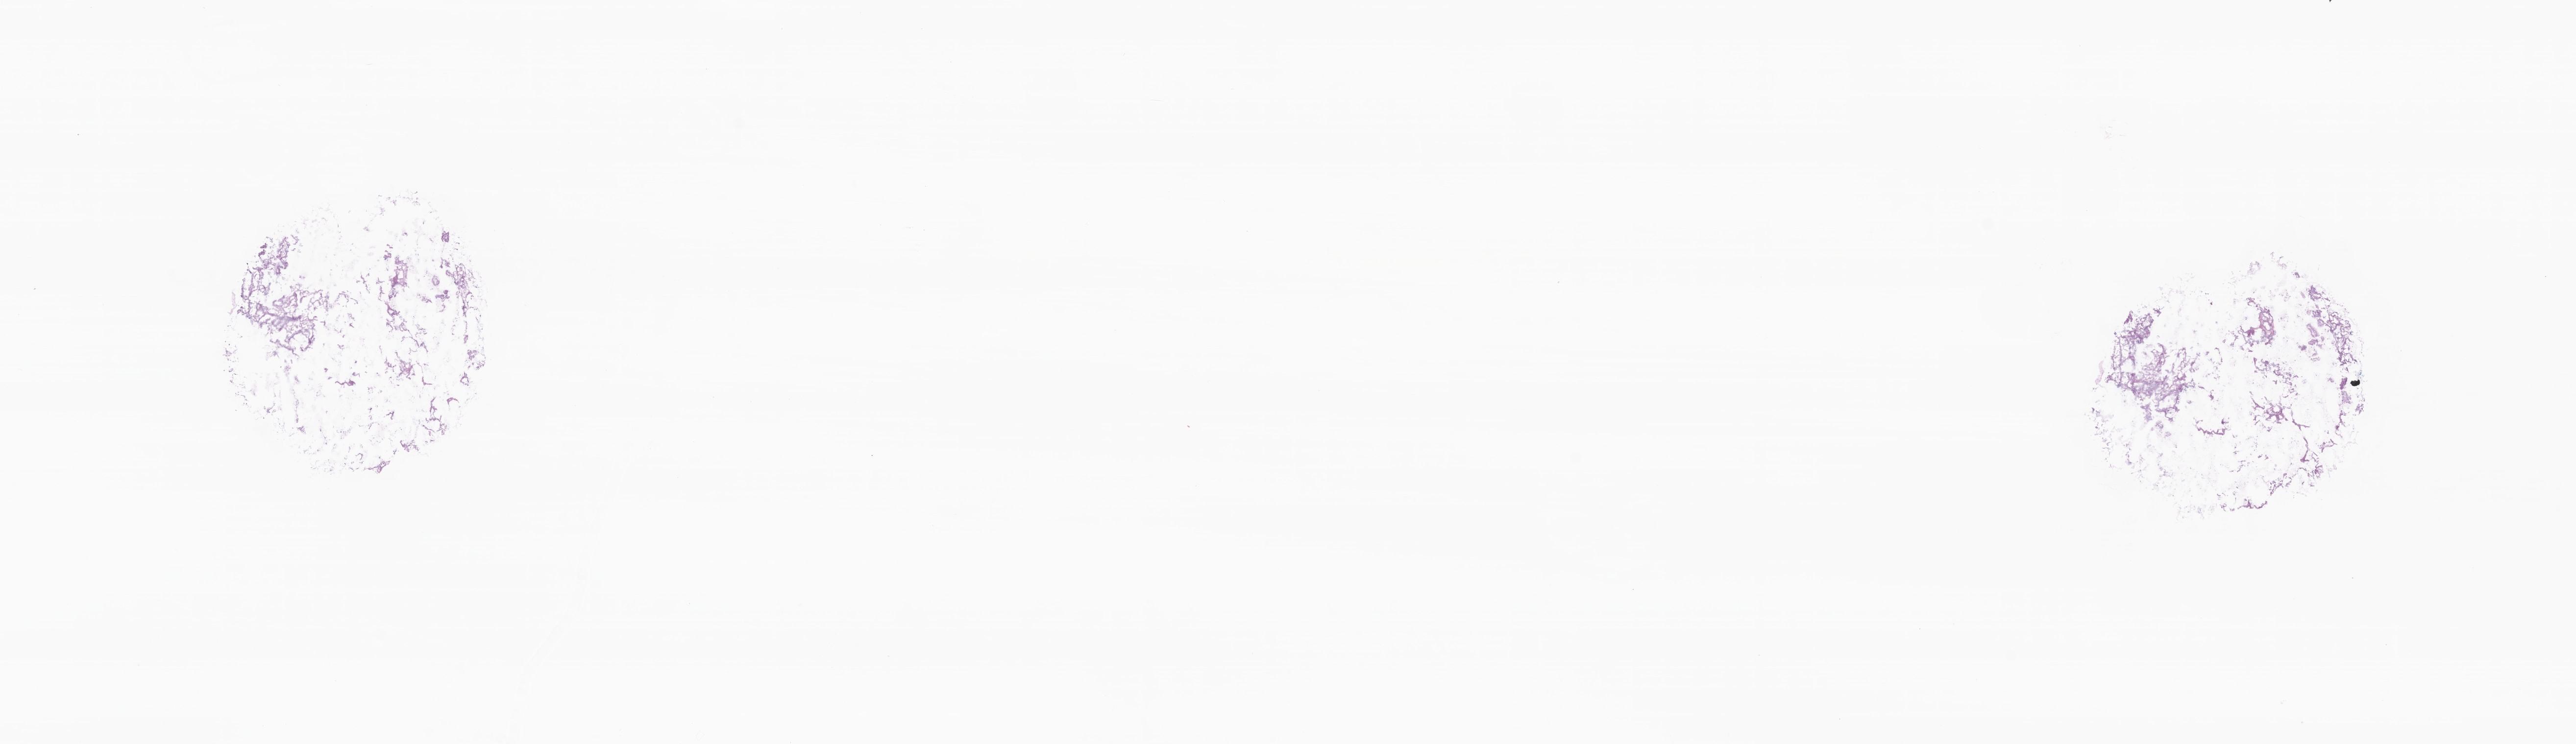
Hematoxylin and eosin (H&E) whole-slide image, low-resolution overview of the scanned area, about 22.2 x 6.4 mm. Frozen section. Primary tumor. Site: middle lobe of right lung. Male patient; age at initial diagnosis 76 years. Slide review estimates, as recorded: tumor cells 70%, tumor nuclei 80%, stromal cells 25%, necrosis 0%, normal cells 5%. Infiltration values recorded for this section: lymphocyte infiltration 0%, monocyte infiltration 0%, neutrophil infiltration 0%.
• diagnosis: Minimally invasive adenocarcinoma, mucinous
• section: top of the tissue portion